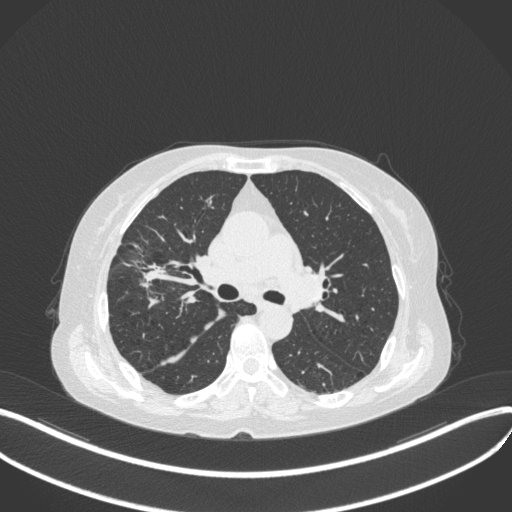
Chest CT, one axial slice. Slice 248 of 429 in the series (ordered by position). Lung window (W 1500 / L -600 HU). 1 mm slice thickness. 512 × 512 image matrix. Female patient, age 69 years. Case-level facts recorded for this patient, not image findings: clinical TNM (as recorded): T1b N3 M0.
Annotated regions visible in this slice (bounding box drawn by a radiologist):
- lung tumour (recorded histology: small cell carcinoma): box from (x=130, y=250) to (x=174, y=286) px